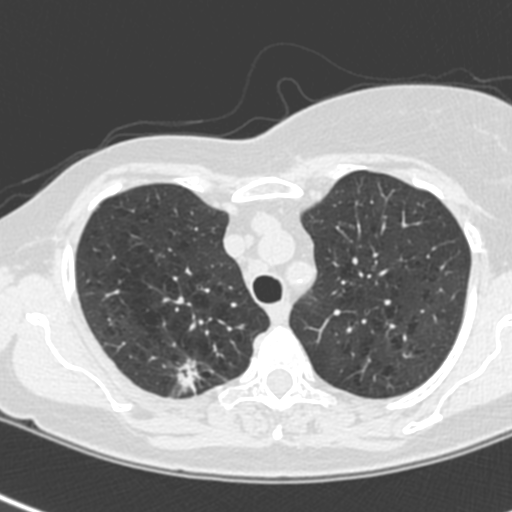
Low-dose screening chest CT, one axial slice. Position 174 of 214 along the scan axis. 120 kVp. Lung window (W 1500 / L -600 HU). 1.3 mm slice thickness. 512 × 512 image matrix.
Structures marked on this image (expert manual segmentation):
- lesion 1 (tumor, upper lobe of right lung): bounding box [x1, y1, x2, y2] px = [177, 360, 199, 392]